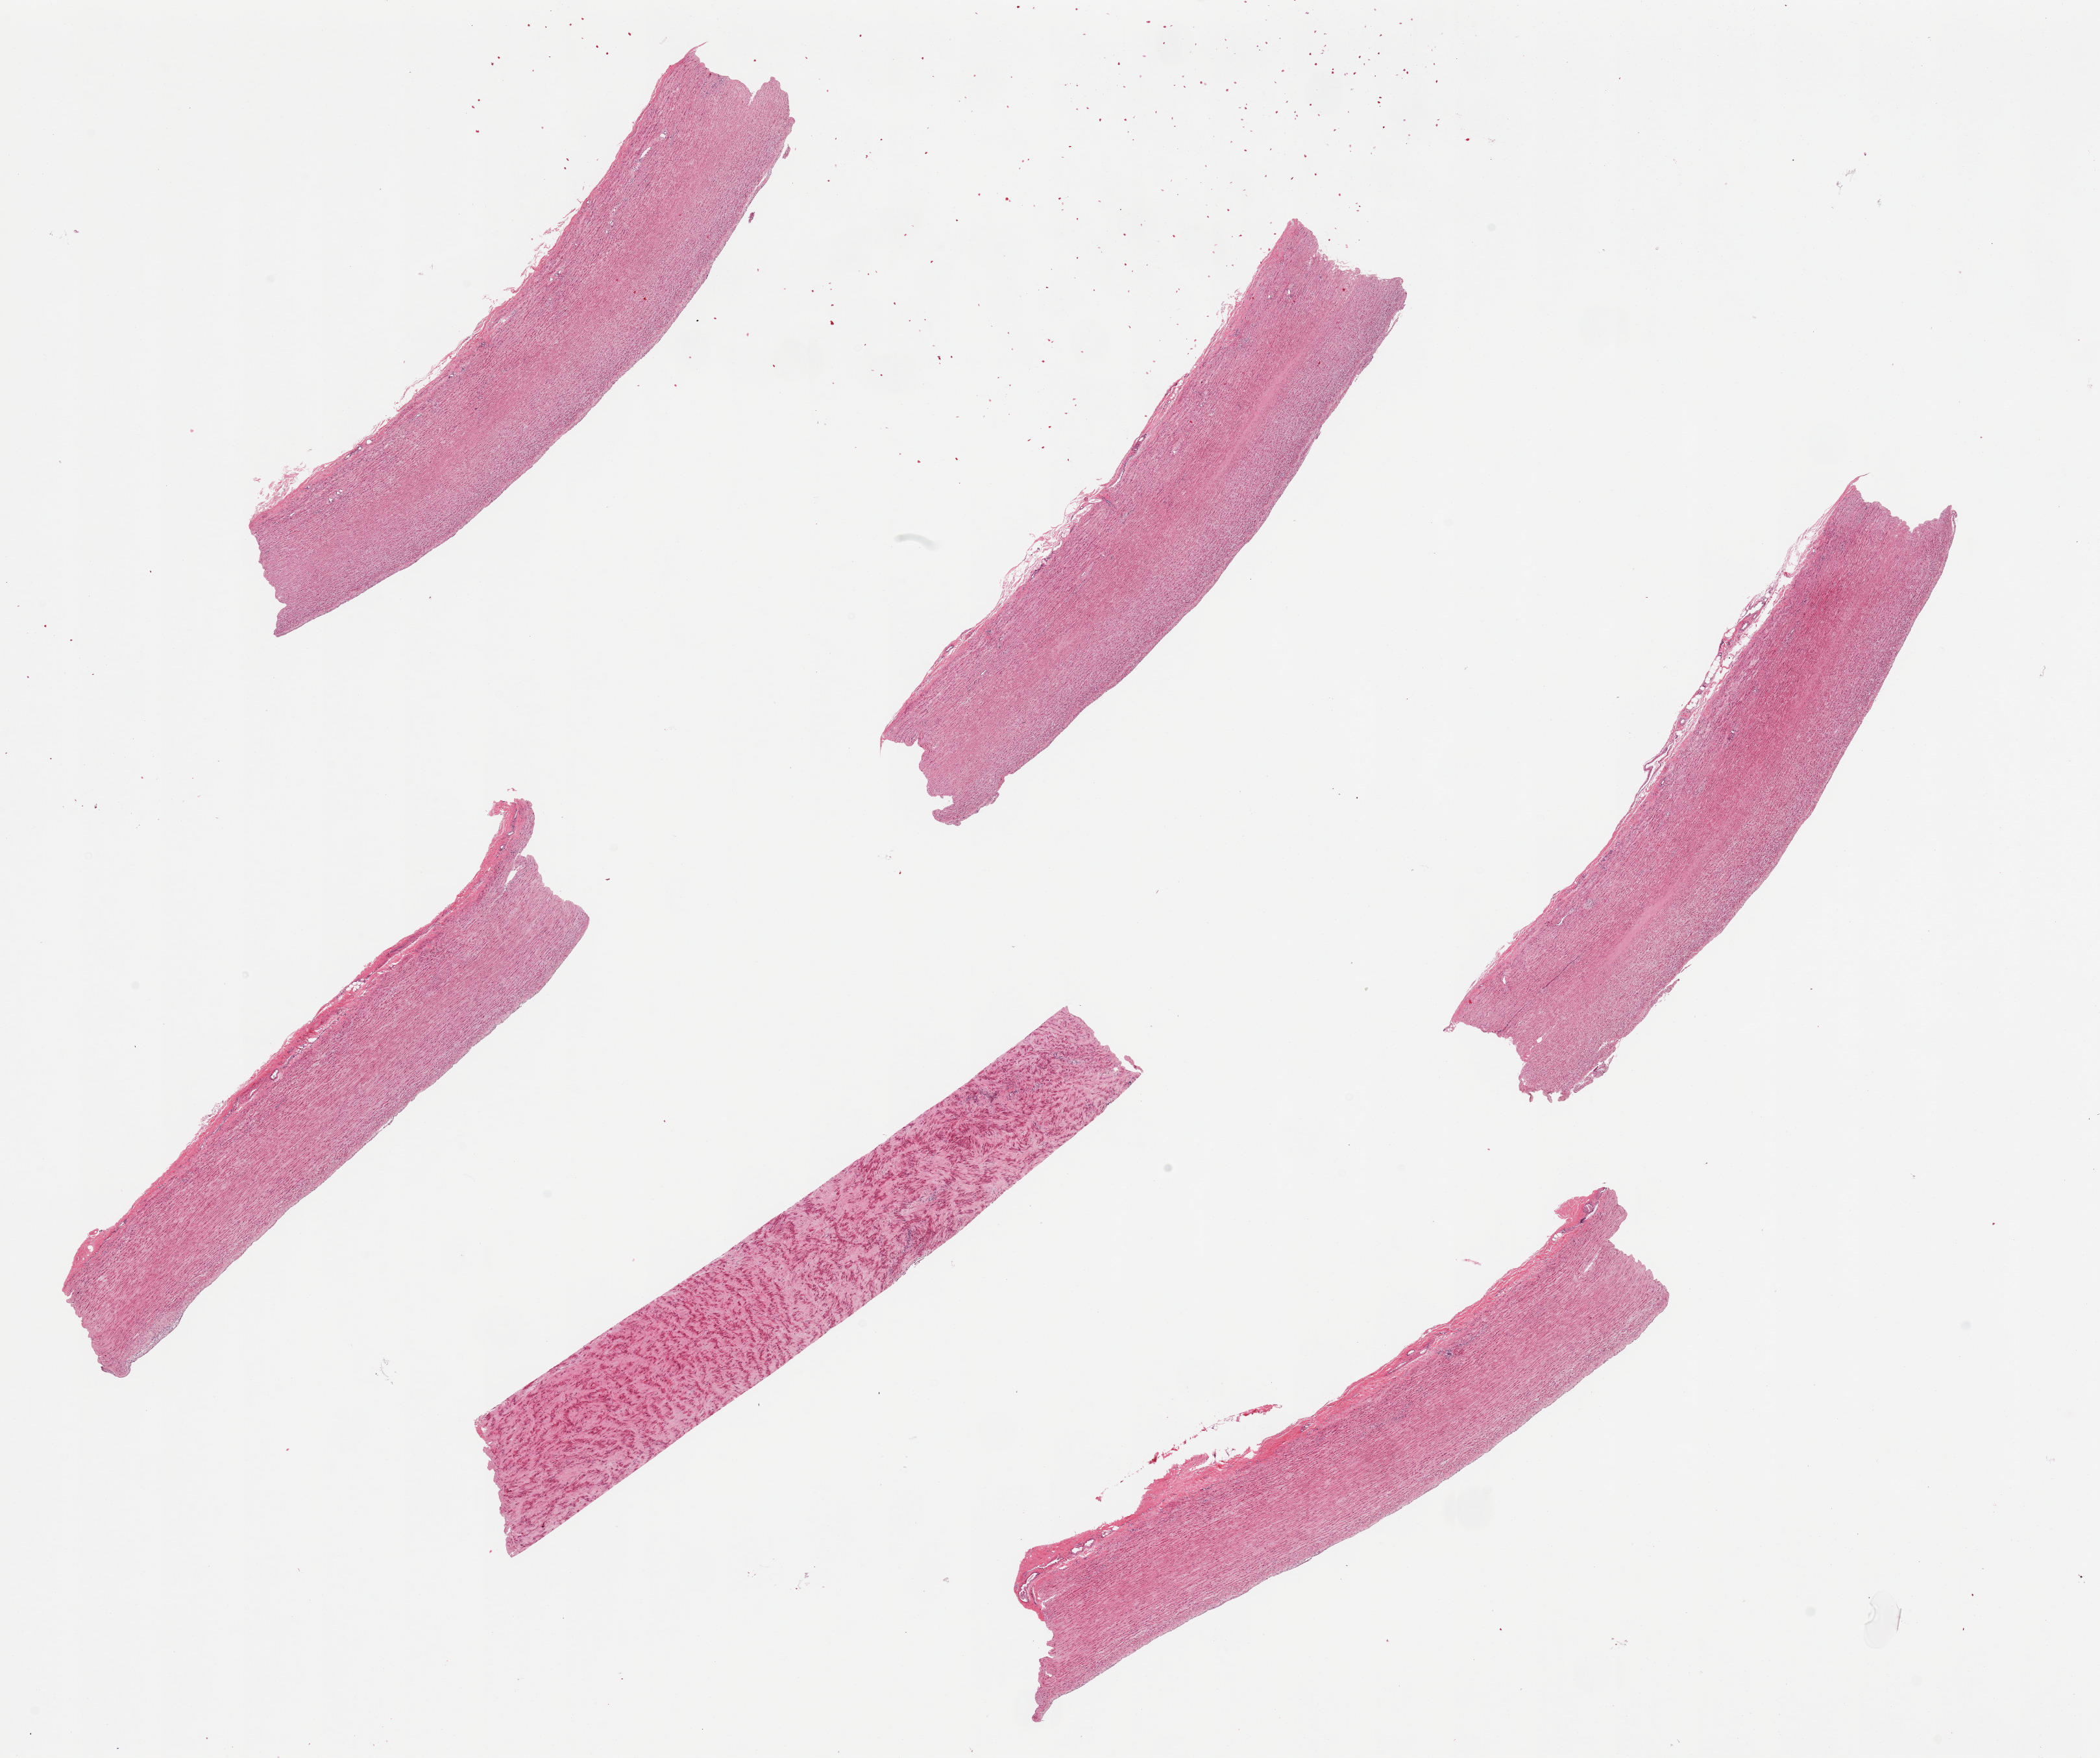
Whole-slide image, hematoxylin and eosin (H&E) stain — whole scanned area (about 25.6 x 21.4 mm) shown as a low-resolution overview, PAXgene-fixed, paraffin-embedded tissue, section of aorta (target tissue), tissue donor sample. Donor sex: male.
• pathologist's review note for this sample: 6 pieces. Well trimmed. No plaques